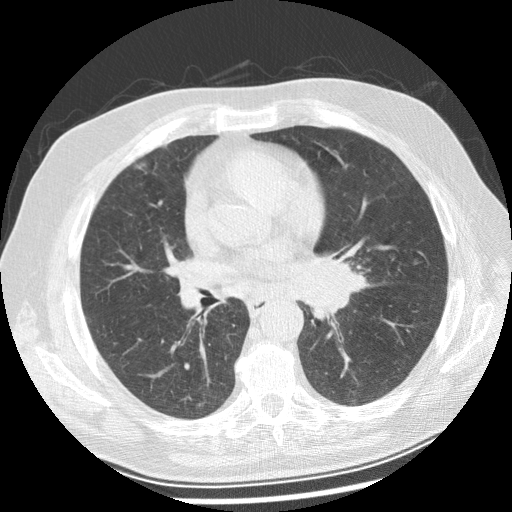
Low-dose screening chest CT, axial slice, baseline screening round, lung window (W 1500 / L -600 HU), 2.5 mm slice thickness, standard (soft-tissue) reconstruction kernel (STANDARD), slice 118 of 250 in the series. Male, age 70 years at enrolment. Current smoker at enrolment.
Lesion marked by an expert reader, bounding box <289,241,372,320> (left, top, right, bottom; pixels). No non-calcified nodule or mass ≥4 mm was recorded by the screening reader at this exam. Later outcome: lung cancer diagnosed 29 days after this screen — squamous cell carcinoma, keratinizing, NOS, left main stem bronchus, moderately differentiated (G2), stage IIIB (AJCC 6th edition), 40 mm at pathology.